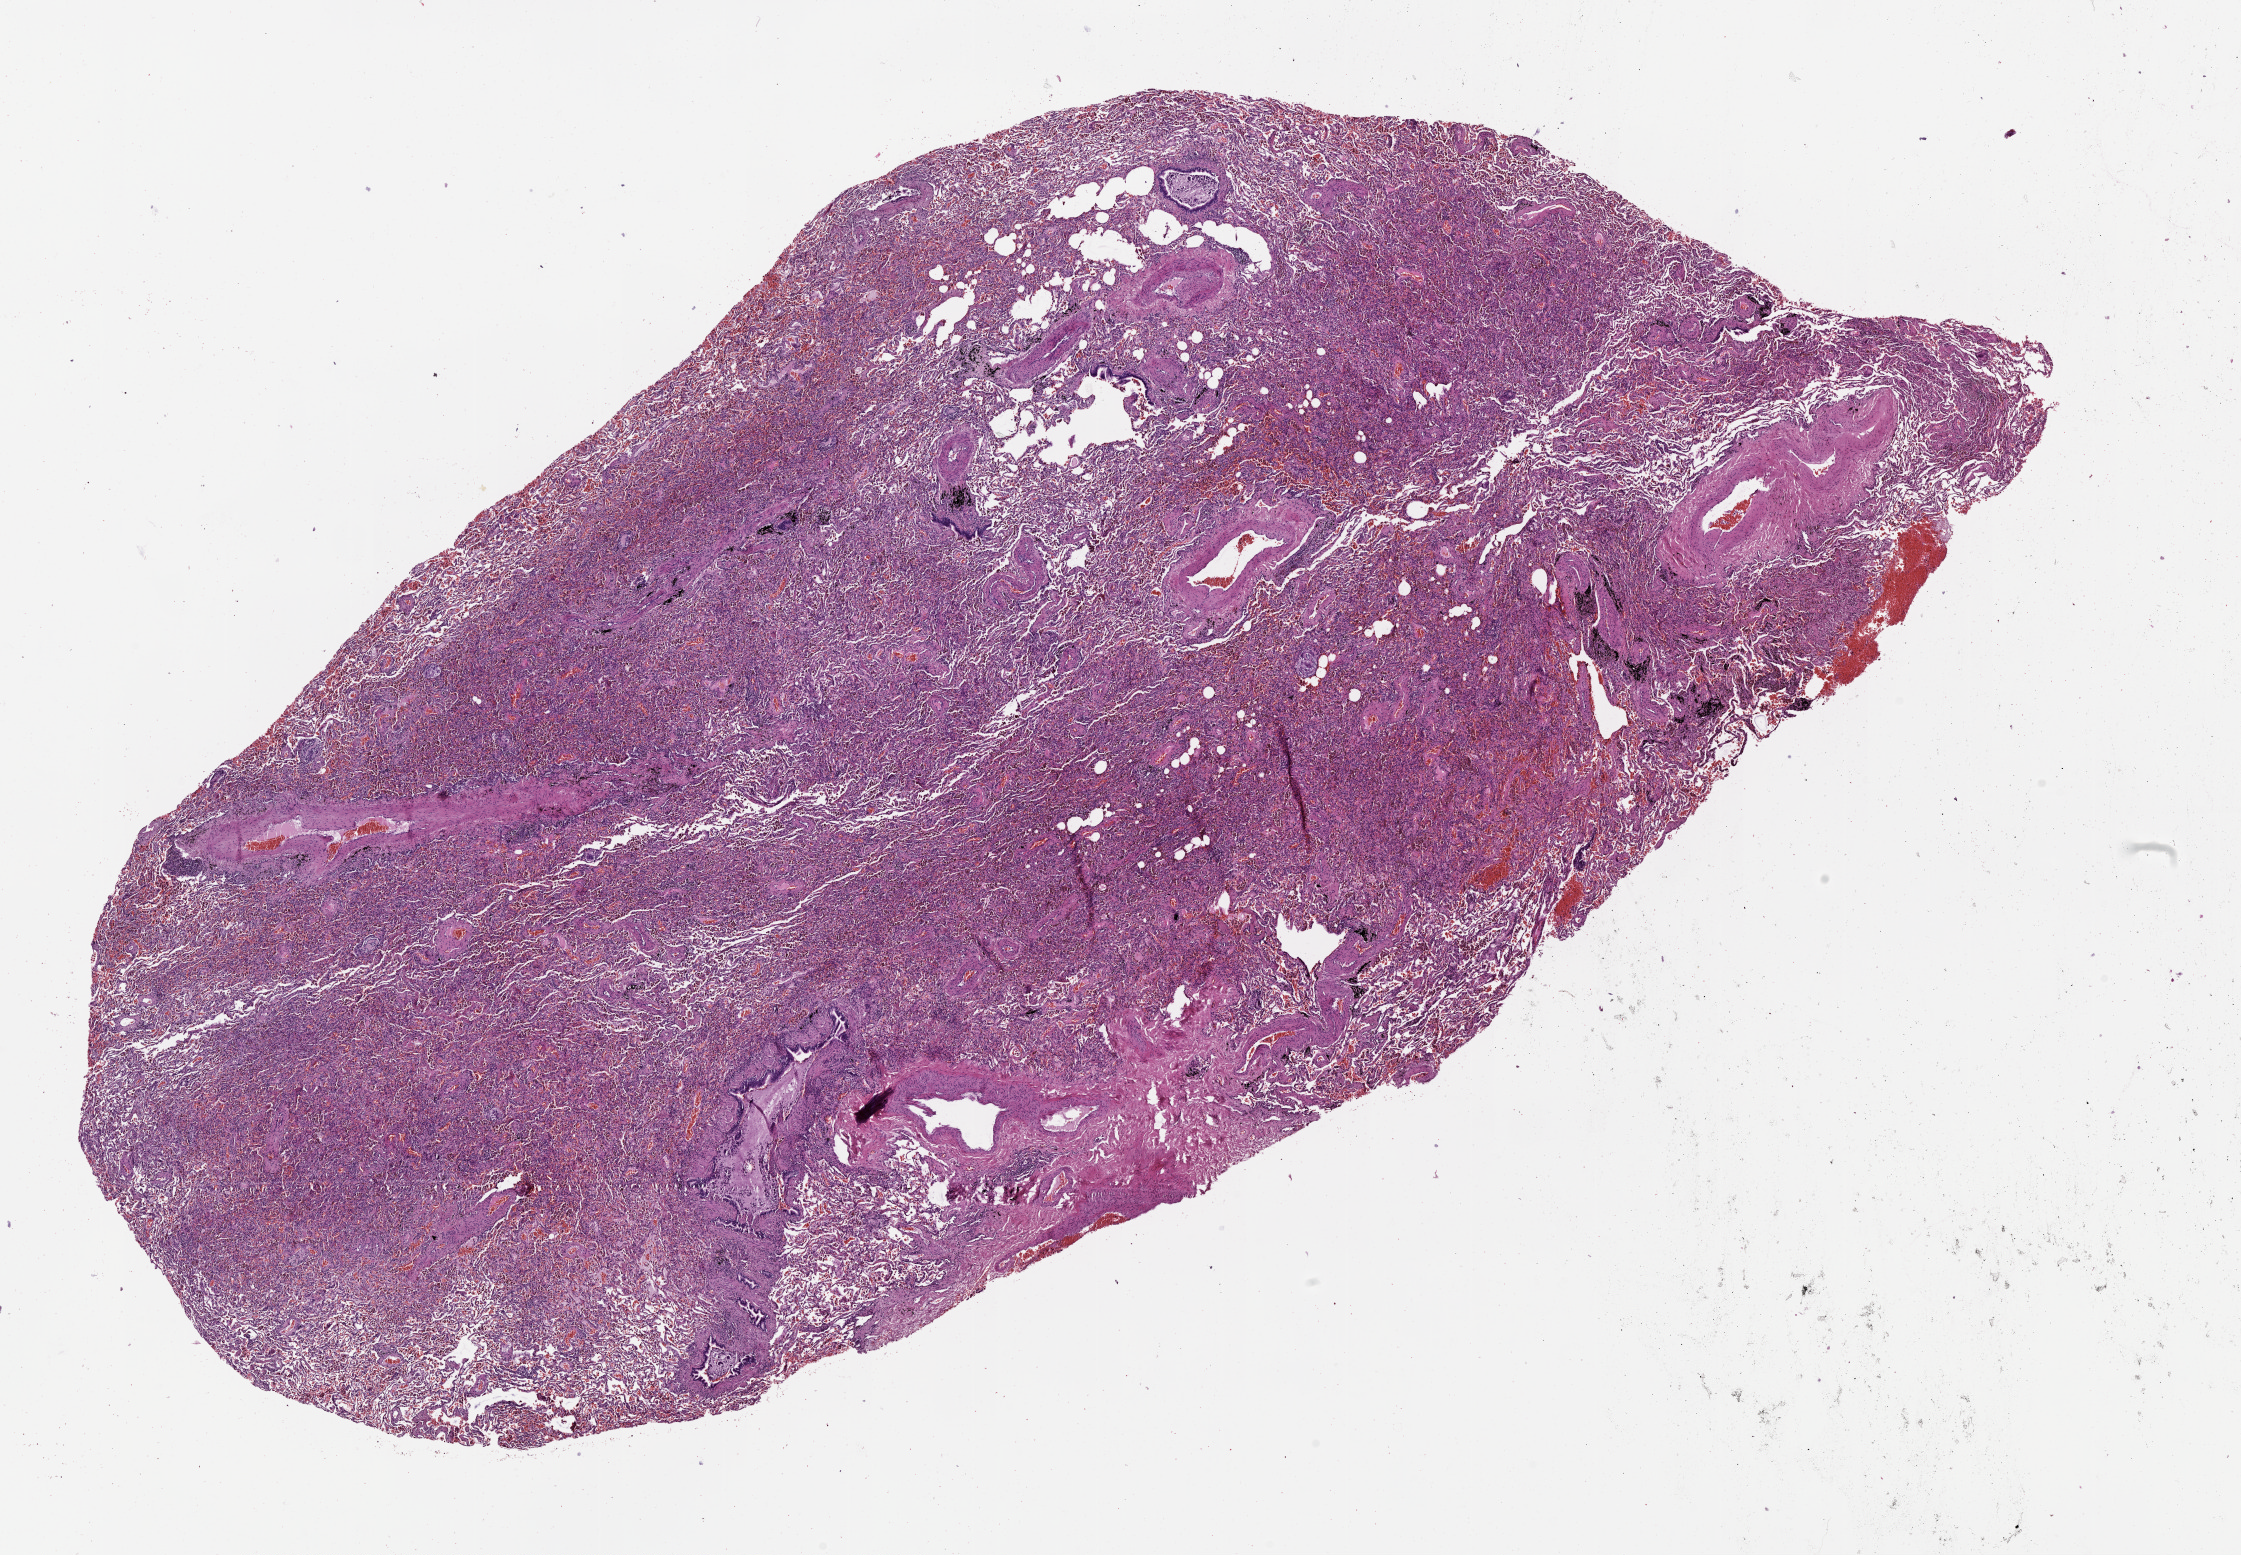
Whole-slide histology image, Hematoxylin and eosin (H&E) stained, shown as a low-resolution overview of the whole scanned area (about 18.0 x 12.5 mm, slide scanned at 20x), lung, normal (non-tumour) tissue. 59-year-old male patient.
This section: normal (non-tumour) tissue from the same patient. Patient diagnosis (cohort enrolment): squamous cell carcinoma (lung).